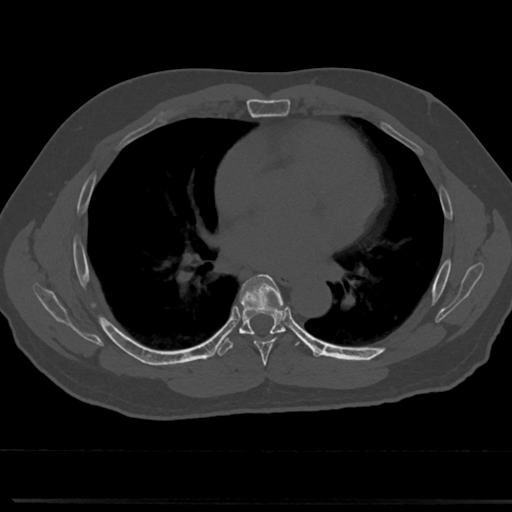
CT including the spine, one axial slice; slice 427 of 817 in the series (ordered by position); 120 kVp; bone window (W 1800 / L 400 HU); 512 × 512 image matrix, field of view 355 × 355 mm. Male patient, age 61 years. From the clinical record (not read from this slice): primary cancer: prostate.
Structures marked on this image (semi-automatically segmented with operator editing):
- T5 vertebra: bounding box [x1, y1, x2, y2] px = [266, 371, 270, 376]
- T6 vertebra: [239, 275, 289, 358]
- T7 vertebra: [240, 325, 285, 335]